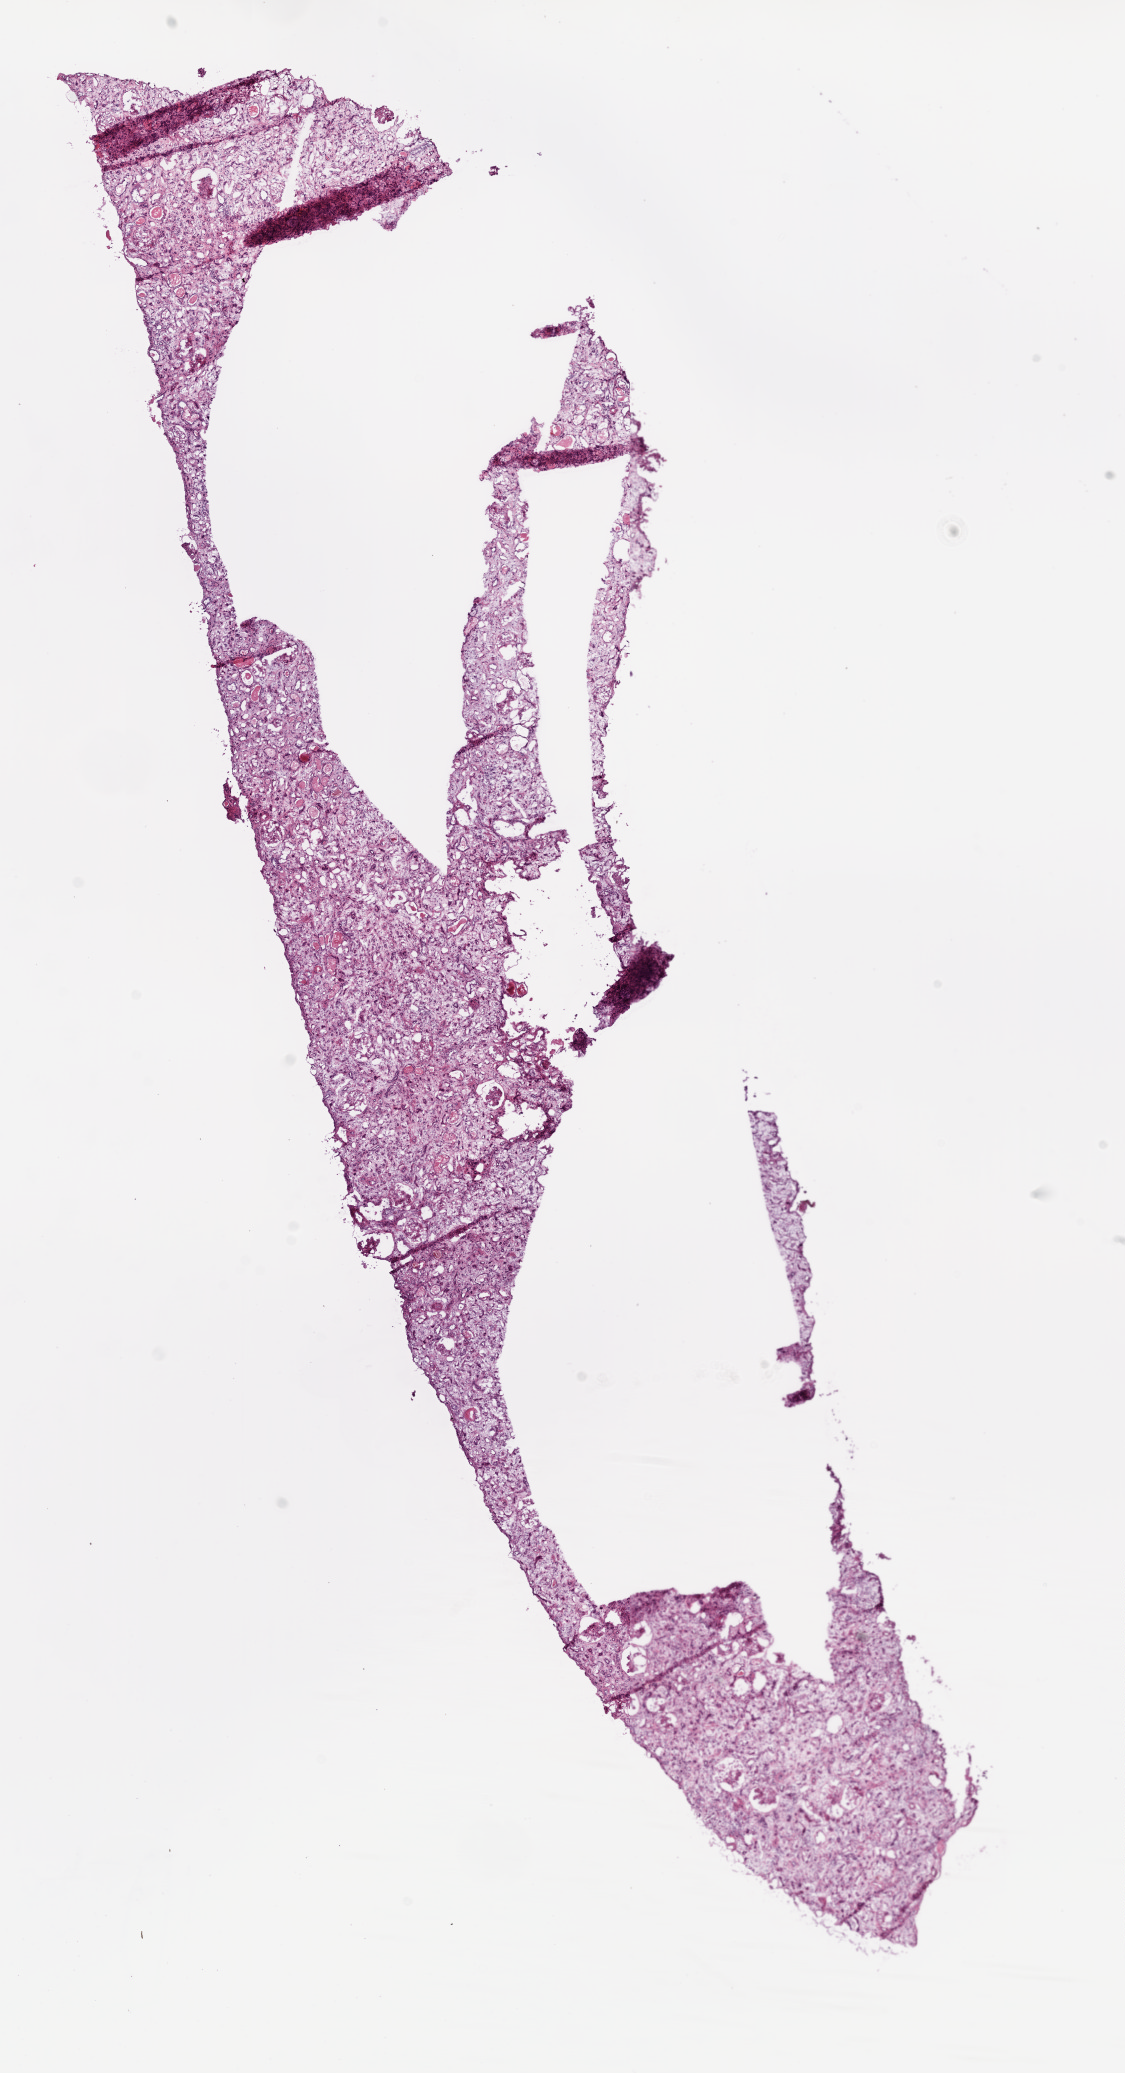
Whole-slide histology image, H&E-stained — shown as a low-resolution overview of the whole scanned area (about 9.0 x 16.6 mm, slide scanned at 20x). Frozen section from the bottom of the tissue portion. Sample: solid tissue normal (non-tumour tissue), kidney. Male, age 60 years at initial diagnosis.
This section: solid tissue normal sample (biorepository sample class). Patient diagnosis: Clear cell adenocarcinoma, NOS.